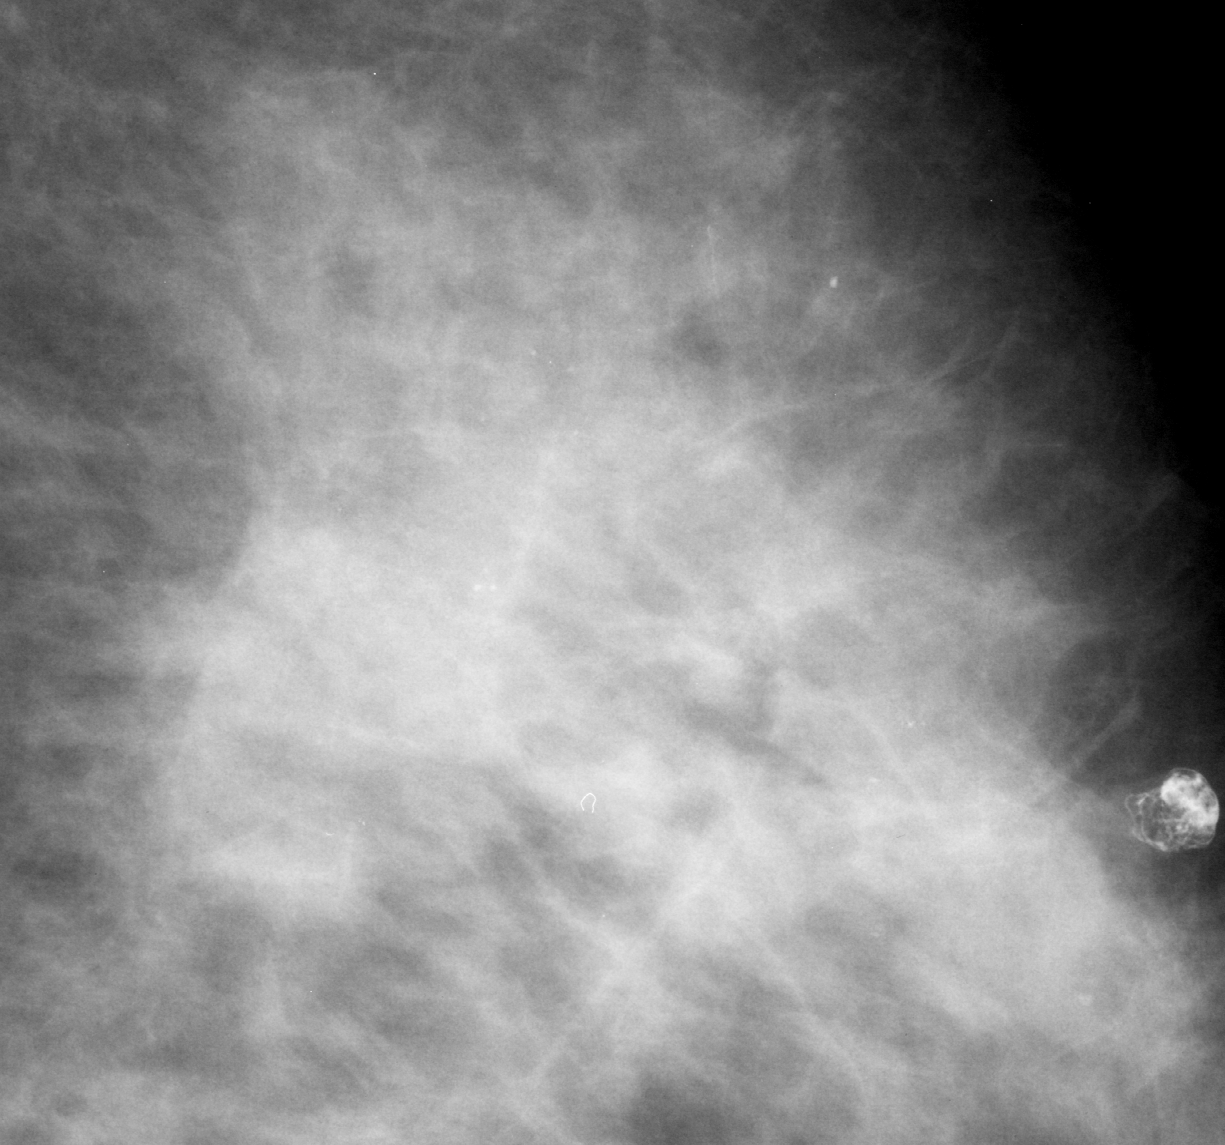
Cropped region of a digitized screen-film mammogram centred on a radiologist-marked abnormality, left breast, MLO view.
Marked abnormality: calcifications, morphology punctate, distribution segmental; BI-RADS assessment category 4; subtlety rating 2 on a 1 (subtle) to 5 (obvious) scale; pathology result (as recorded, not read from the image): malignant.